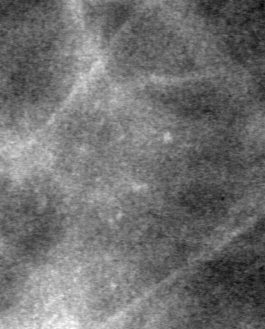
Crop from a digitized film mammogram around one marked abnormality; left breast; CC view.
Finding: calcifications, morphology pleomorphic, distribution clustered; BI-RADS assessment category 4; subtlety rating 1 on a 1 (subtle) to 5 (obvious) scale; pathology result (as recorded, not read from the image): benign.